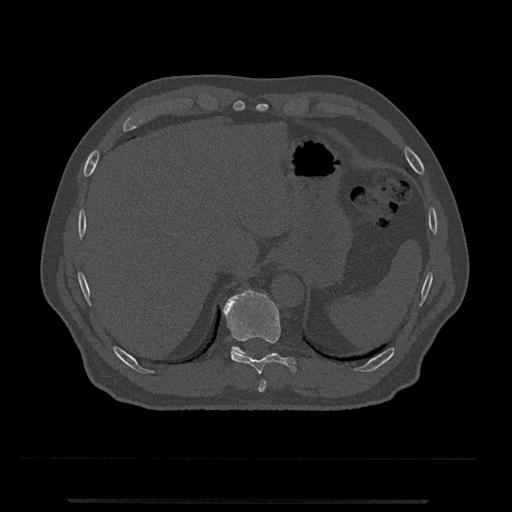
CT including the spine, one axial slice; position 510 of 797 along the scan axis; 120 kVp; bone window (W 1800 / L 400 HU); 512 × 512 image matrix, field of view 419 × 419 mm. Patient: male, 63 years. From the clinical record (not read from this slice): primary cancer: prostate.
Structures marked on this image (semi-automatic segmentation, software-assisted and operator-edited):
- T10 vertebra: bounding box <223,289,297,374> (left, top, right, bottom; pixels)
- T11 vertebra: <231,346,273,356>
- T9 vertebra: <258,380,267,392>